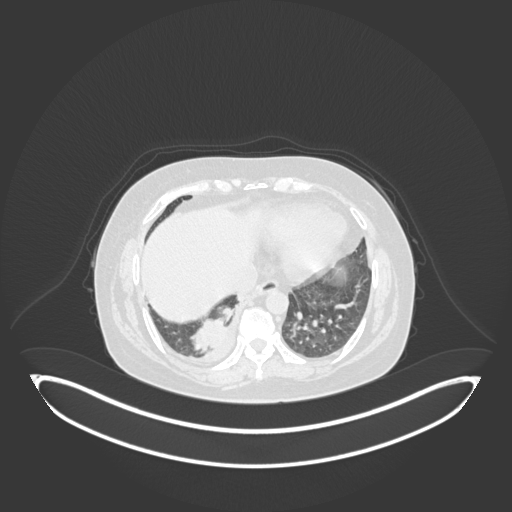
Chest CT, one axial slice. Position 35 of 231 along the scan axis. Reconstruction kernel B30f. 120 kVp. Lung window (W 1500 / L -600 HU). 1 mm slice thickness. 512 × 512 image matrix. Female patient, age 56 years. Case-level facts recorded for this patient, not image findings: clinical TNM (as recorded): T2b N1 M0; histopathological grade: G3.
Outlined on this slice (rectangle marked by the reading radiologist):
- lung tumour (recorded histology: small cell carcinoma): bounding box (x1, y1, x2, y2) in pixels: (186, 300, 233, 356)